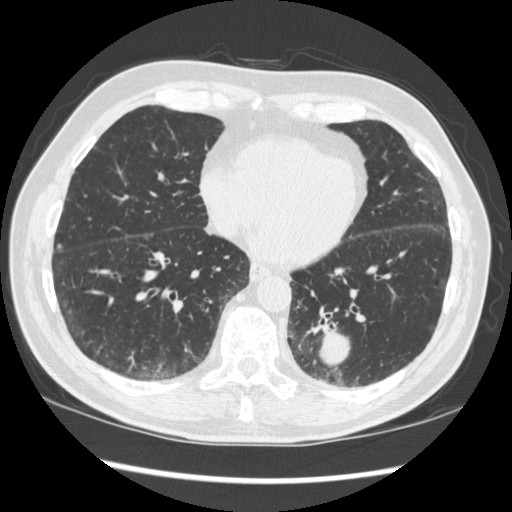
Low-dose screening chest CT, one axial slice. Slice 116 of 348 in the series (ordered by position). Reconstruction kernel STANDARD. Lung window (W 1500 / L -600 HU). 1.25 mm slice thickness. 512 × 512 image matrix, field of view 360 × 360 mm.
Outlined on this slice (outlined manually by an expert reader):
- lesion 1 (tumor, lower lobe of left lung): bounding box [x1, y1, x2, y2] px = [319, 325, 349, 367]